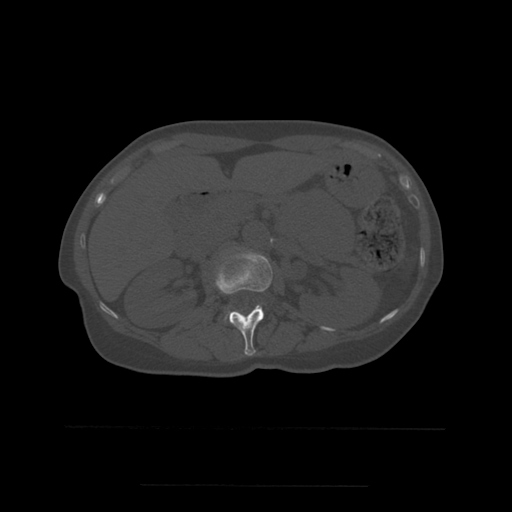
CT including the spine, one axial slice. Slice 228 of 544 in the series (ordered by position). Bone window (W 1800 / L 400 HU). 512 × 512 image matrix, field of view 350 × 350 mm. Patient age 58 years. Case-level facts recorded for this patient, not image findings: primary cancer: lung.
Structures marked on this image (semi-automatically segmented with operator editing):
- L1 vertebra: bounding box [x1, y1, x2, y2] px = [215, 252, 273, 356]
- L2 vertebra: [227, 311, 231, 319]